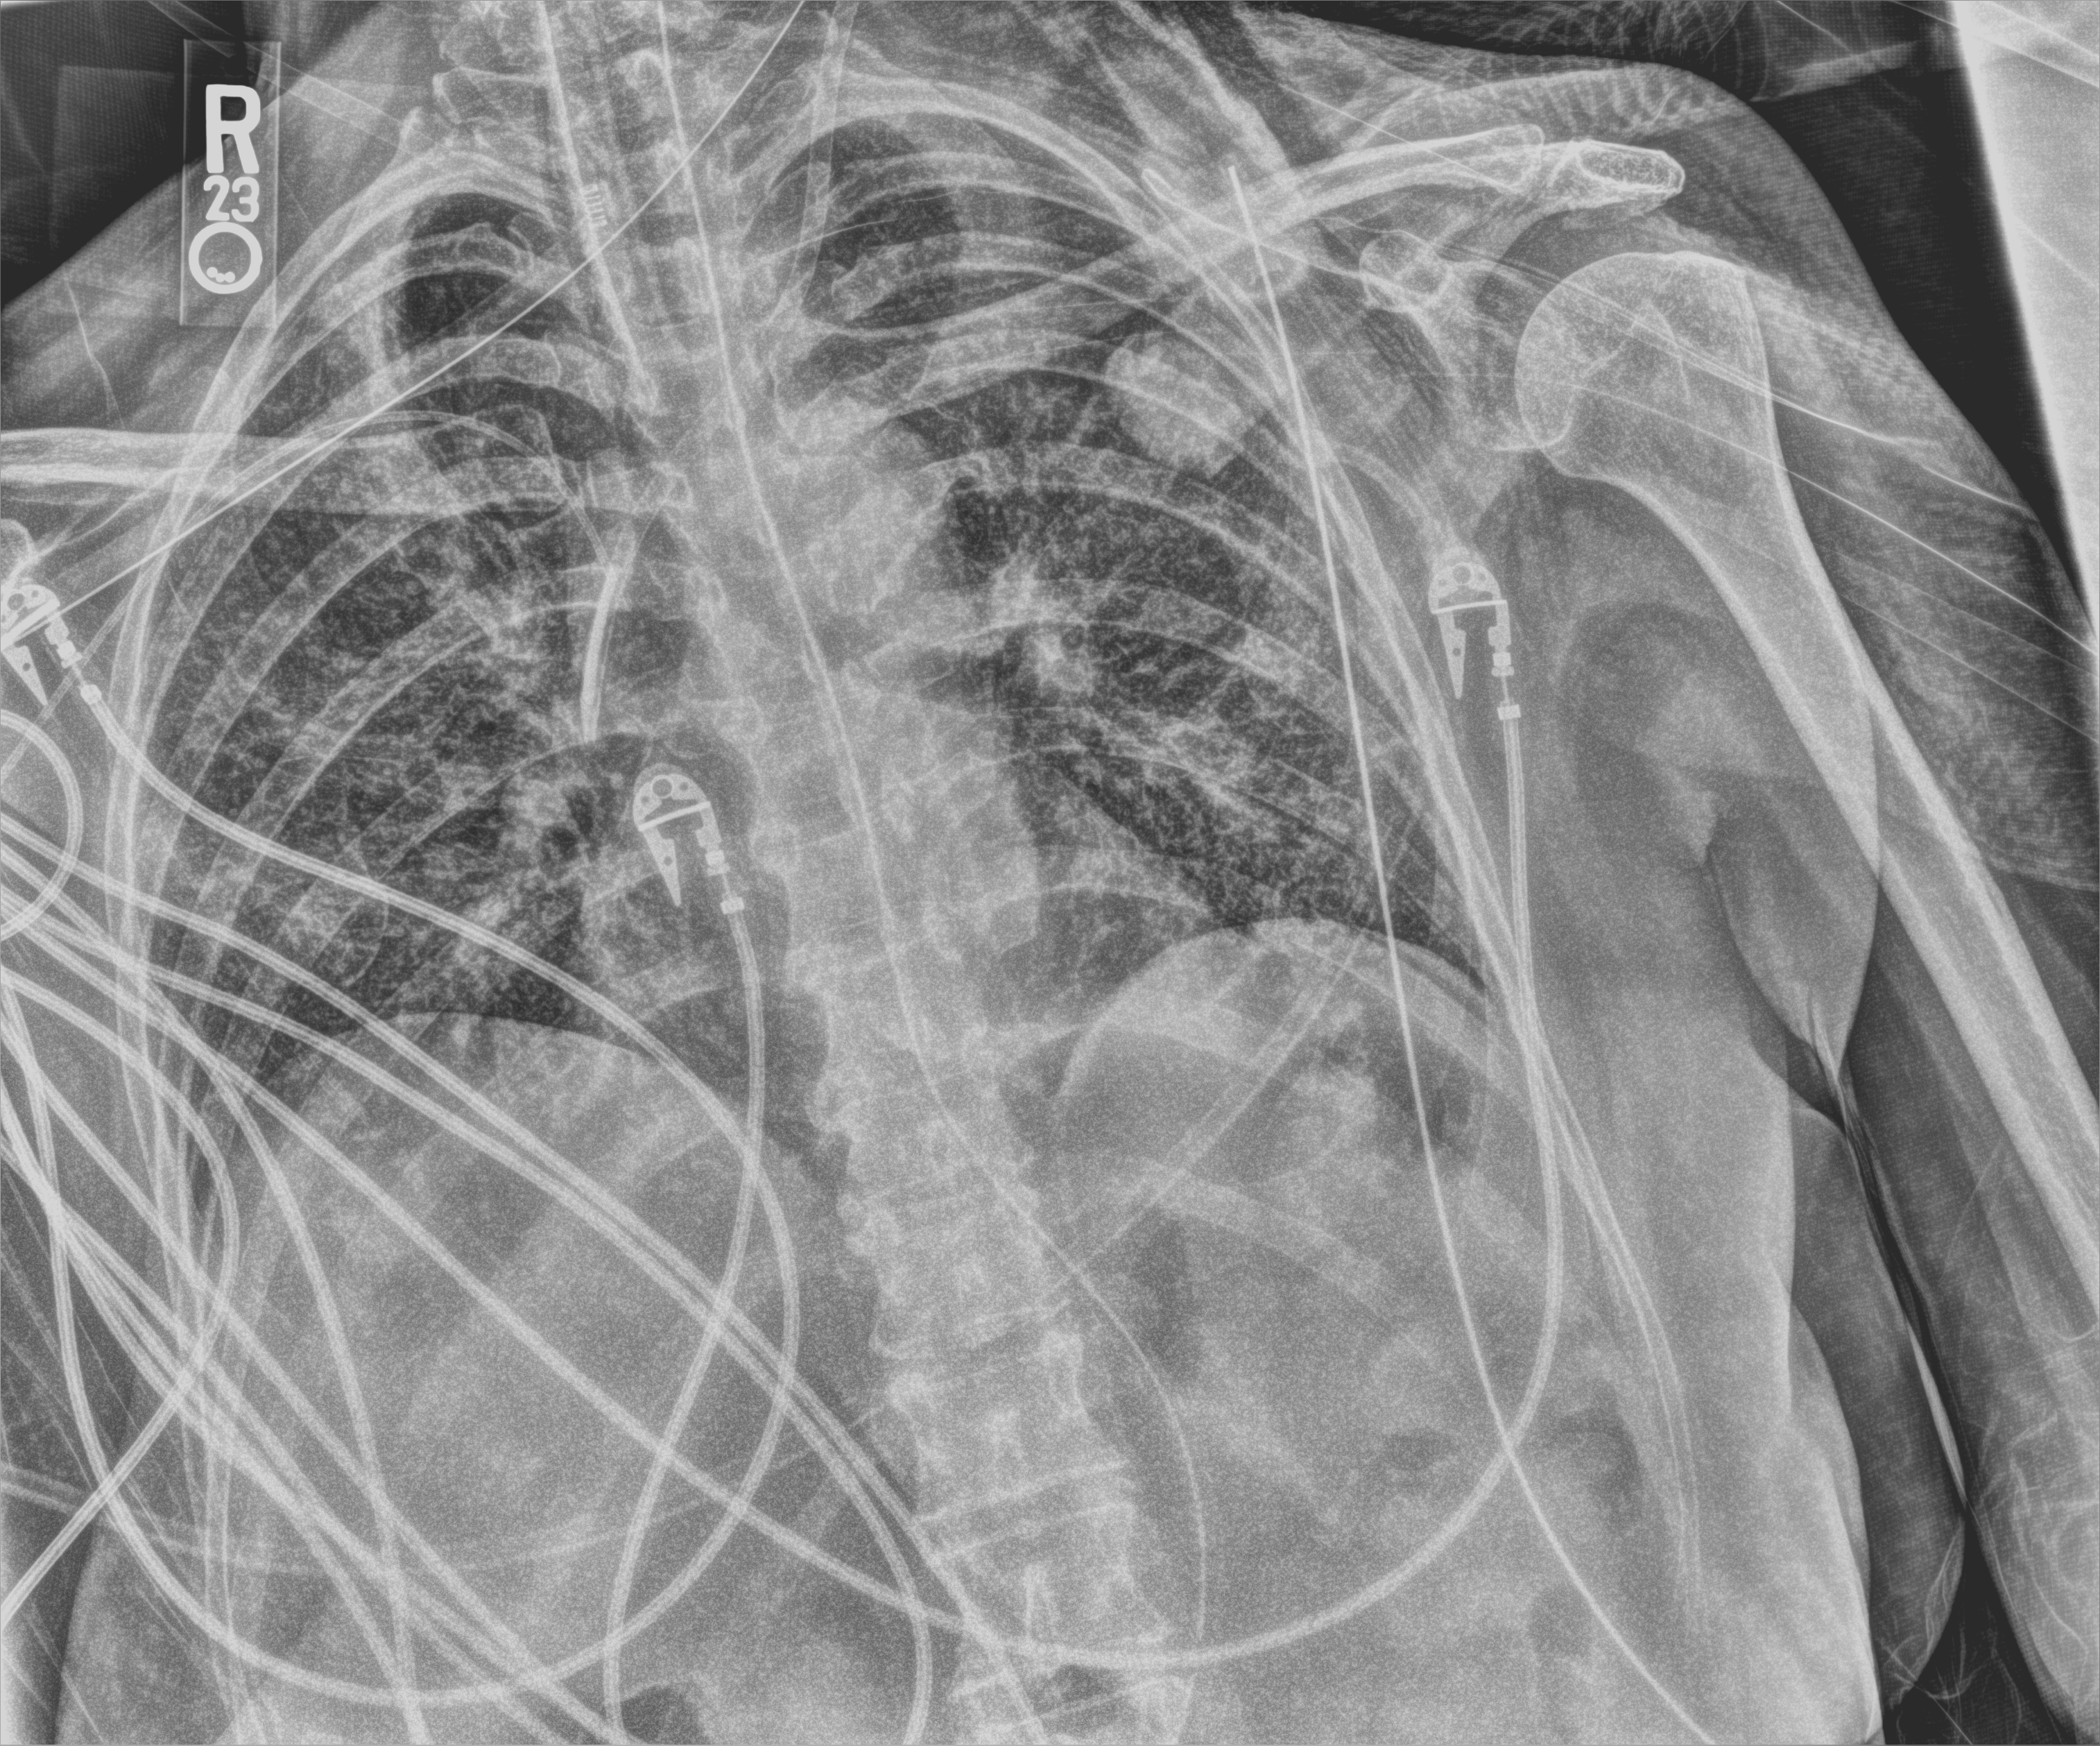
Chest X-ray (portable); anteroposterior (AP) projection. Patient hospitalised with COVID-19; female, aged 60–74 years.
Hospital-stay facts (about this admission, not read from this image; timing relative to this image not recorded):
- mechanically ventilated during this hospital stay: yes
- admitted to intensive care during this hospital stay: yes